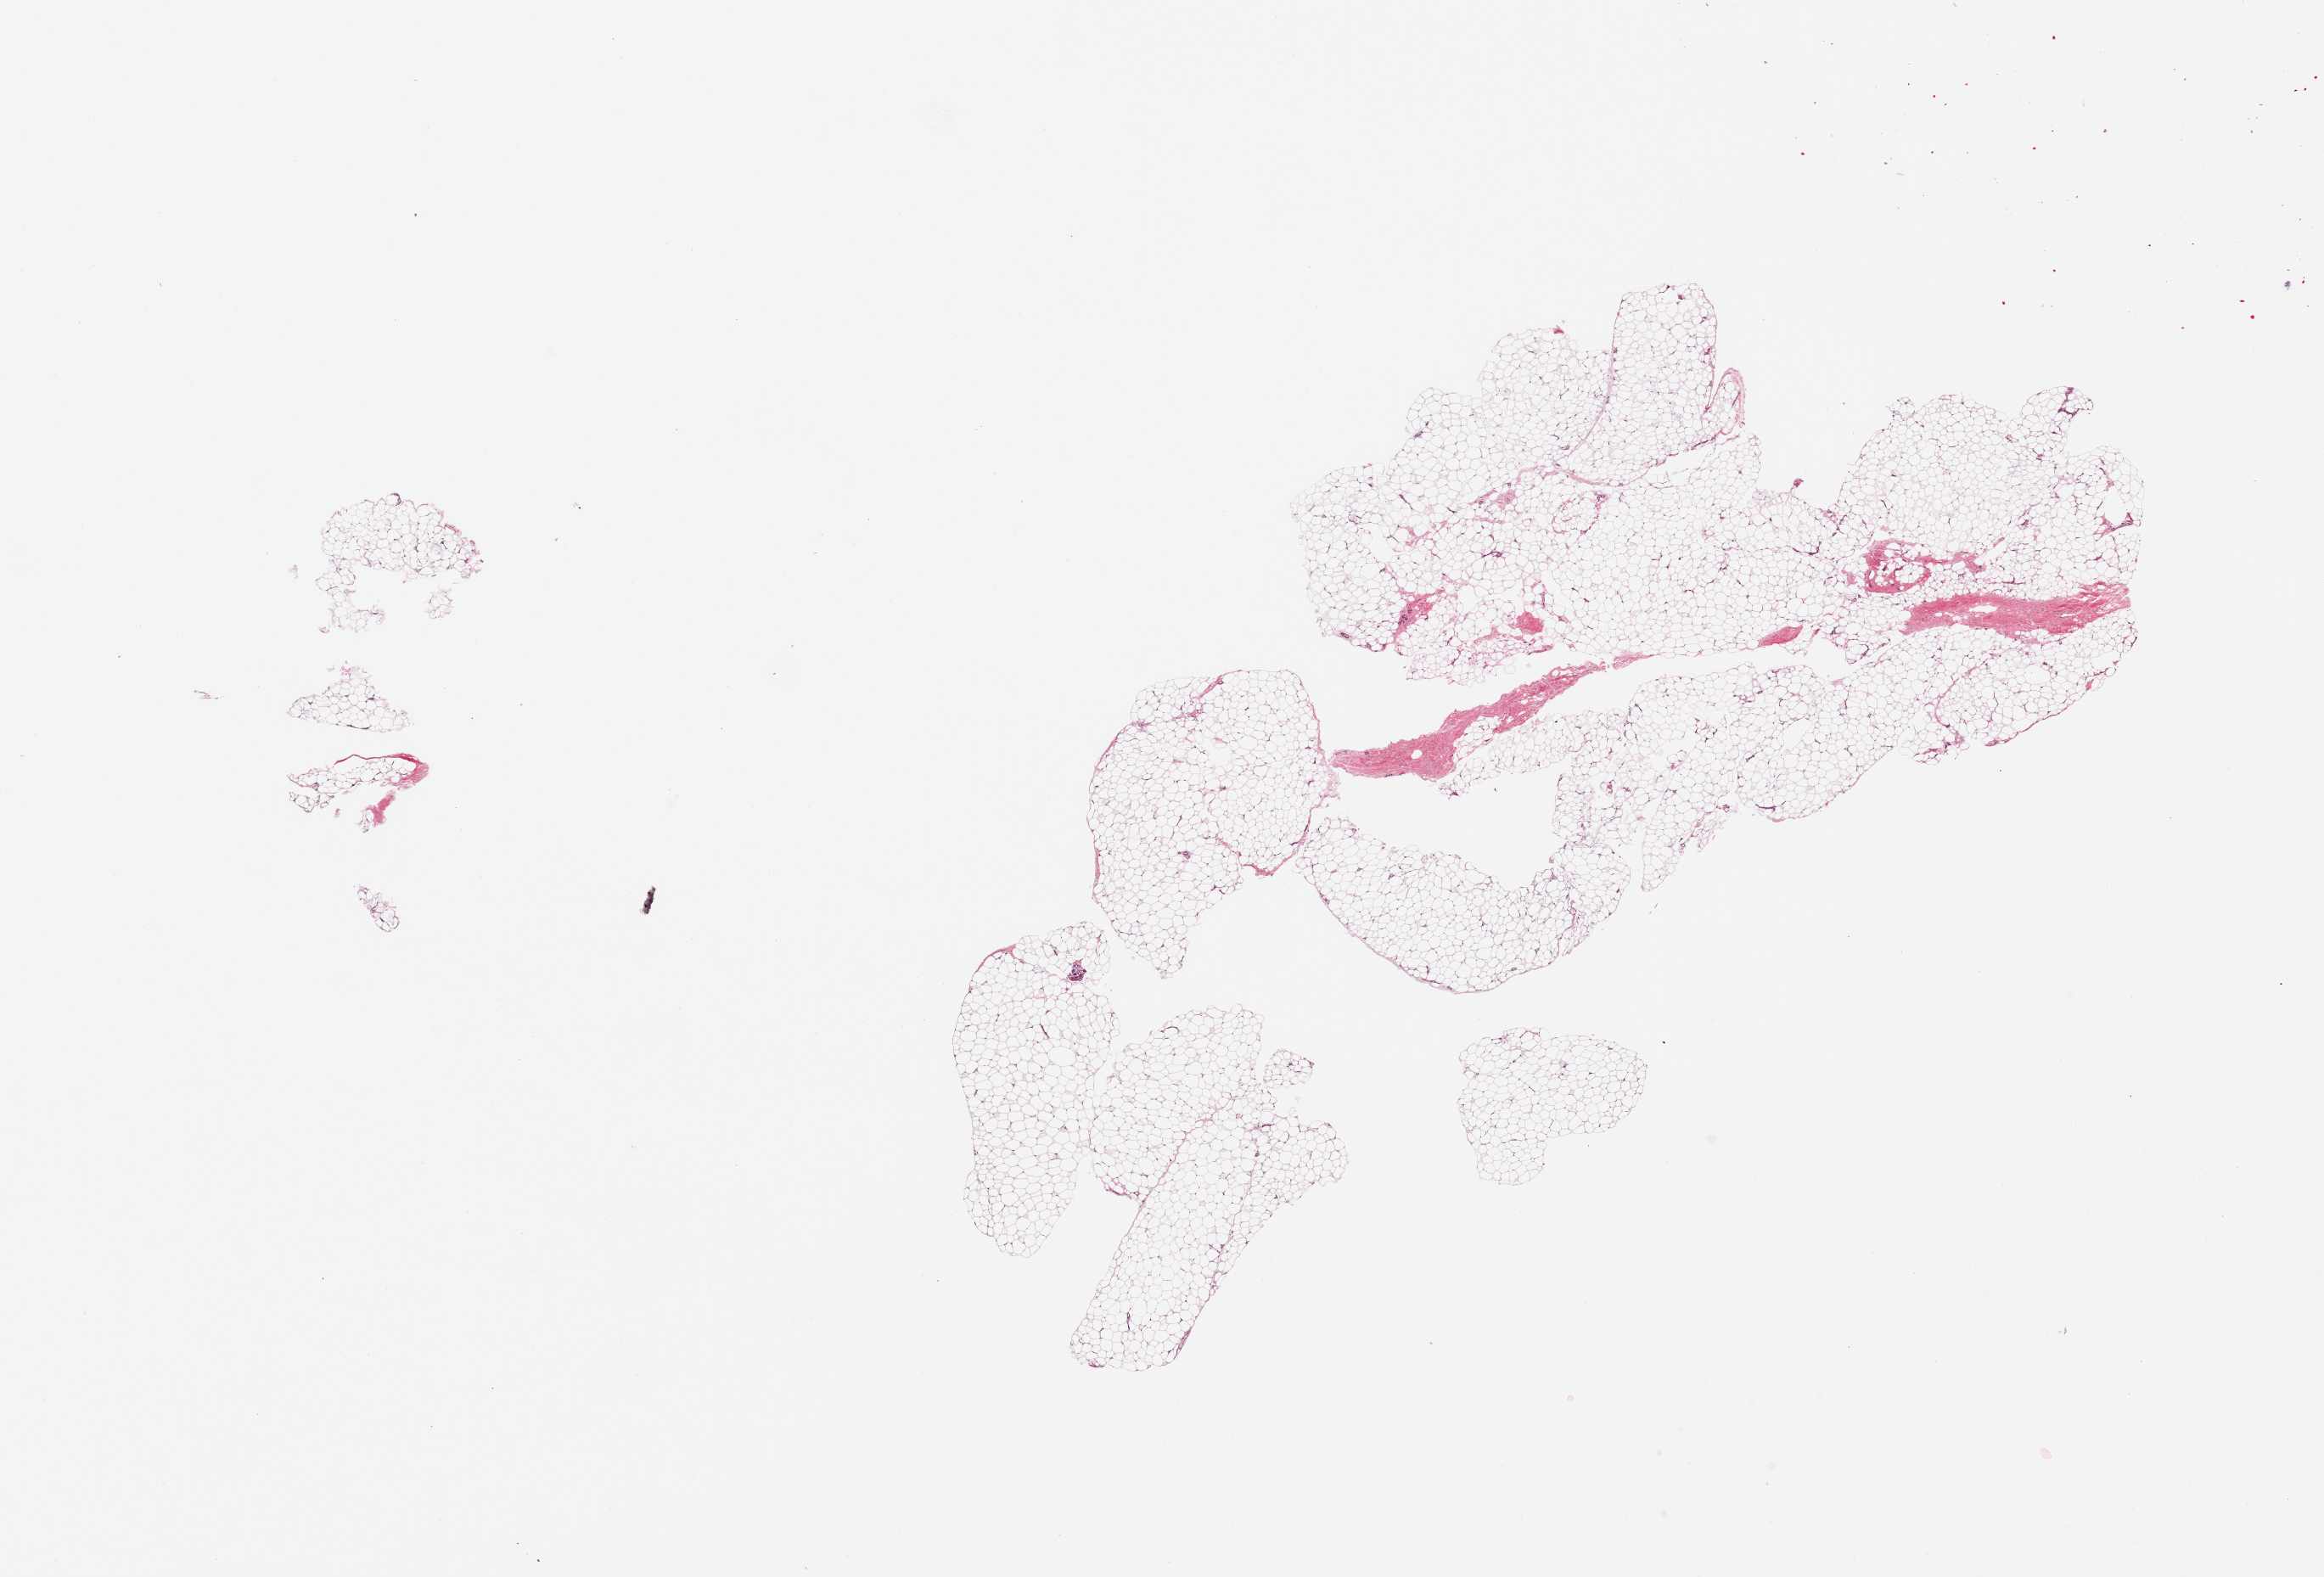
Hematoxylin and eosin (H&E) whole-slide image, brightfield — a low-resolution overview of the entire scanned area, about 21.7 x 14.7 mm (slide scanned at 20x), PAXgene-fixed paraffin-embedded (PFPE) section, section of adipose tissue (target tissue), donor tissue sample. Donor sex: male.
Pathologist's review note for this sample: 1 piece + small fragment; ~10% fascia.